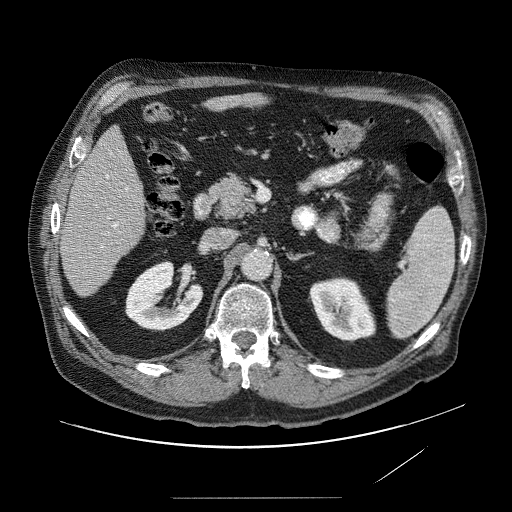
Contrast-enhanced abdominal CT (liver protocol), one axial slice. Slice 28 of 89 in the series (ordered by position). Reconstruction kernel STANDARD. Soft-tissue window (W 400 / L 40 HU). 512 × 512 image matrix, field of view 420 × 420 mm. Case-level facts recorded for this patient, not image findings: diagnosis: hepatocellular carcinoma (patient treated with transarterial chemoembolisation; whether this scan precedes or follows treatment is not stated here); TNM stage (as recorded): Stage-IVA; Child-Pugh class: A; tumour nodularity: multinodular.
Structures marked on this image (semi-automatically segmented with operator editing):
- liver parenchyma outside the tumour (the mass and vessels are separate outlines, so this box may not span the whole liver): box from (x=60, y=132) to (x=152, y=300) px
- liver vessels: (x=97, y=166)–(x=138, y=253)